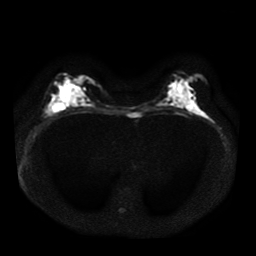
Breast MRI, one axial slice; slice 21 of 41 in the series (ordered by position); diffusion-weighted series; image 2 of 4 stored at this slice position (different b-values; order by instance number); 1.5 T; 5 mm slice thickness; 256 × 256 image matrix, field of view 330 × 330 mm. Female patient.
Outlined on this slice (outlined manually by an expert reader):
- tumour on diffusion-weighted imaging: bounding box (x1, y1, x2, y2) in pixels: (55, 101, 63, 109)